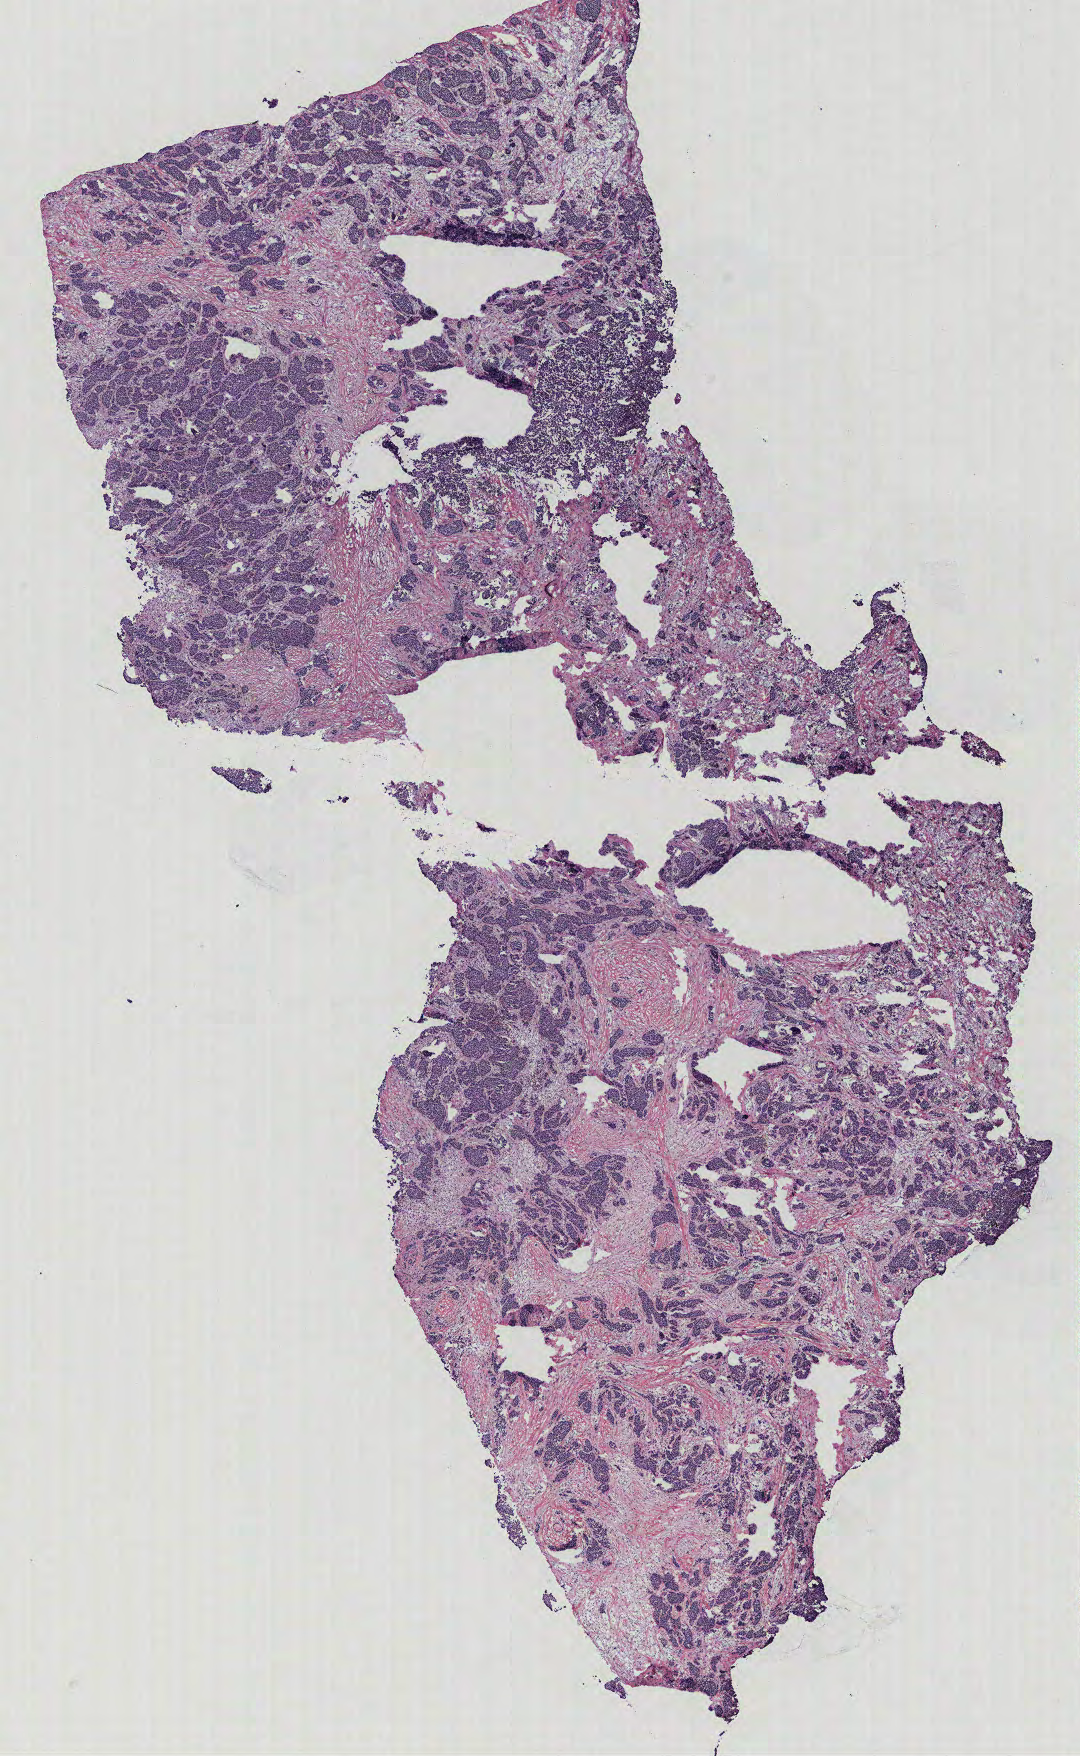
H&E whole-slide image — a low-resolution overview of the entire scanned area, about 8.6 x 14.1 mm (acquisition: 40x scan), breast, tissue type not recorded.
• patient diagnosis (cohort enrolment): breast cancer (breast)